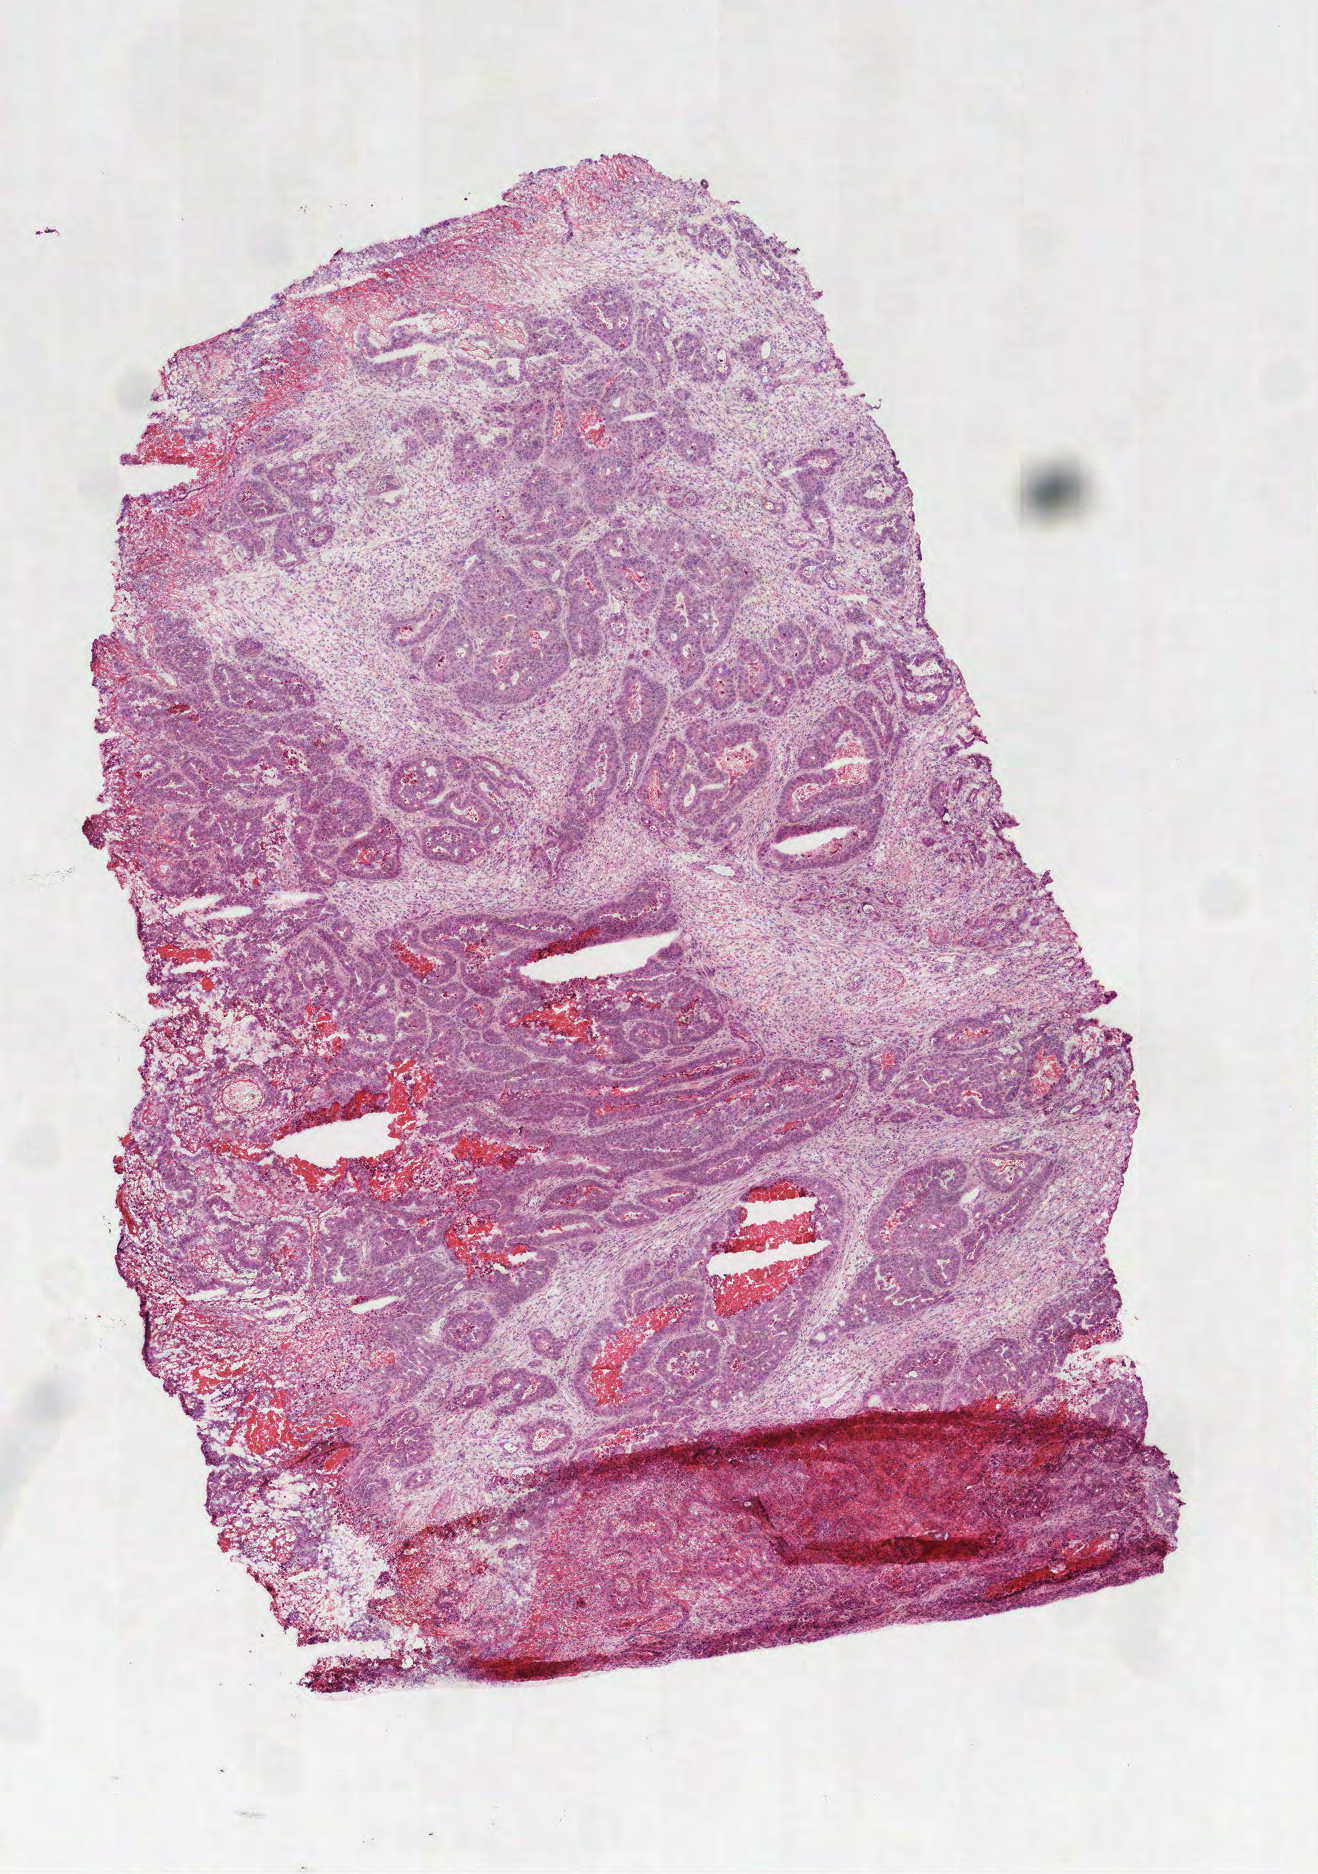
H&E-stained whole-slide image — low-resolution overview of the scanned area, about 5.3 x 7.6 mm; frozen section; primary tumour sample from the stomach. Female, age 70 years at initial diagnosis. Histologic grade: G2 (moderately differentiated). Slide review estimates, as recorded: tumour cells 55%, tumour nuclei 70%, normal cells 0%, stromal cells 30%, necrosis 15%.
Lymph nodes positive (case pathology): 0 of 26 examined. AJCC pathologic stage: IB. Pathologic diagnosis: Tubular adenocarcinoma (body of stomach).